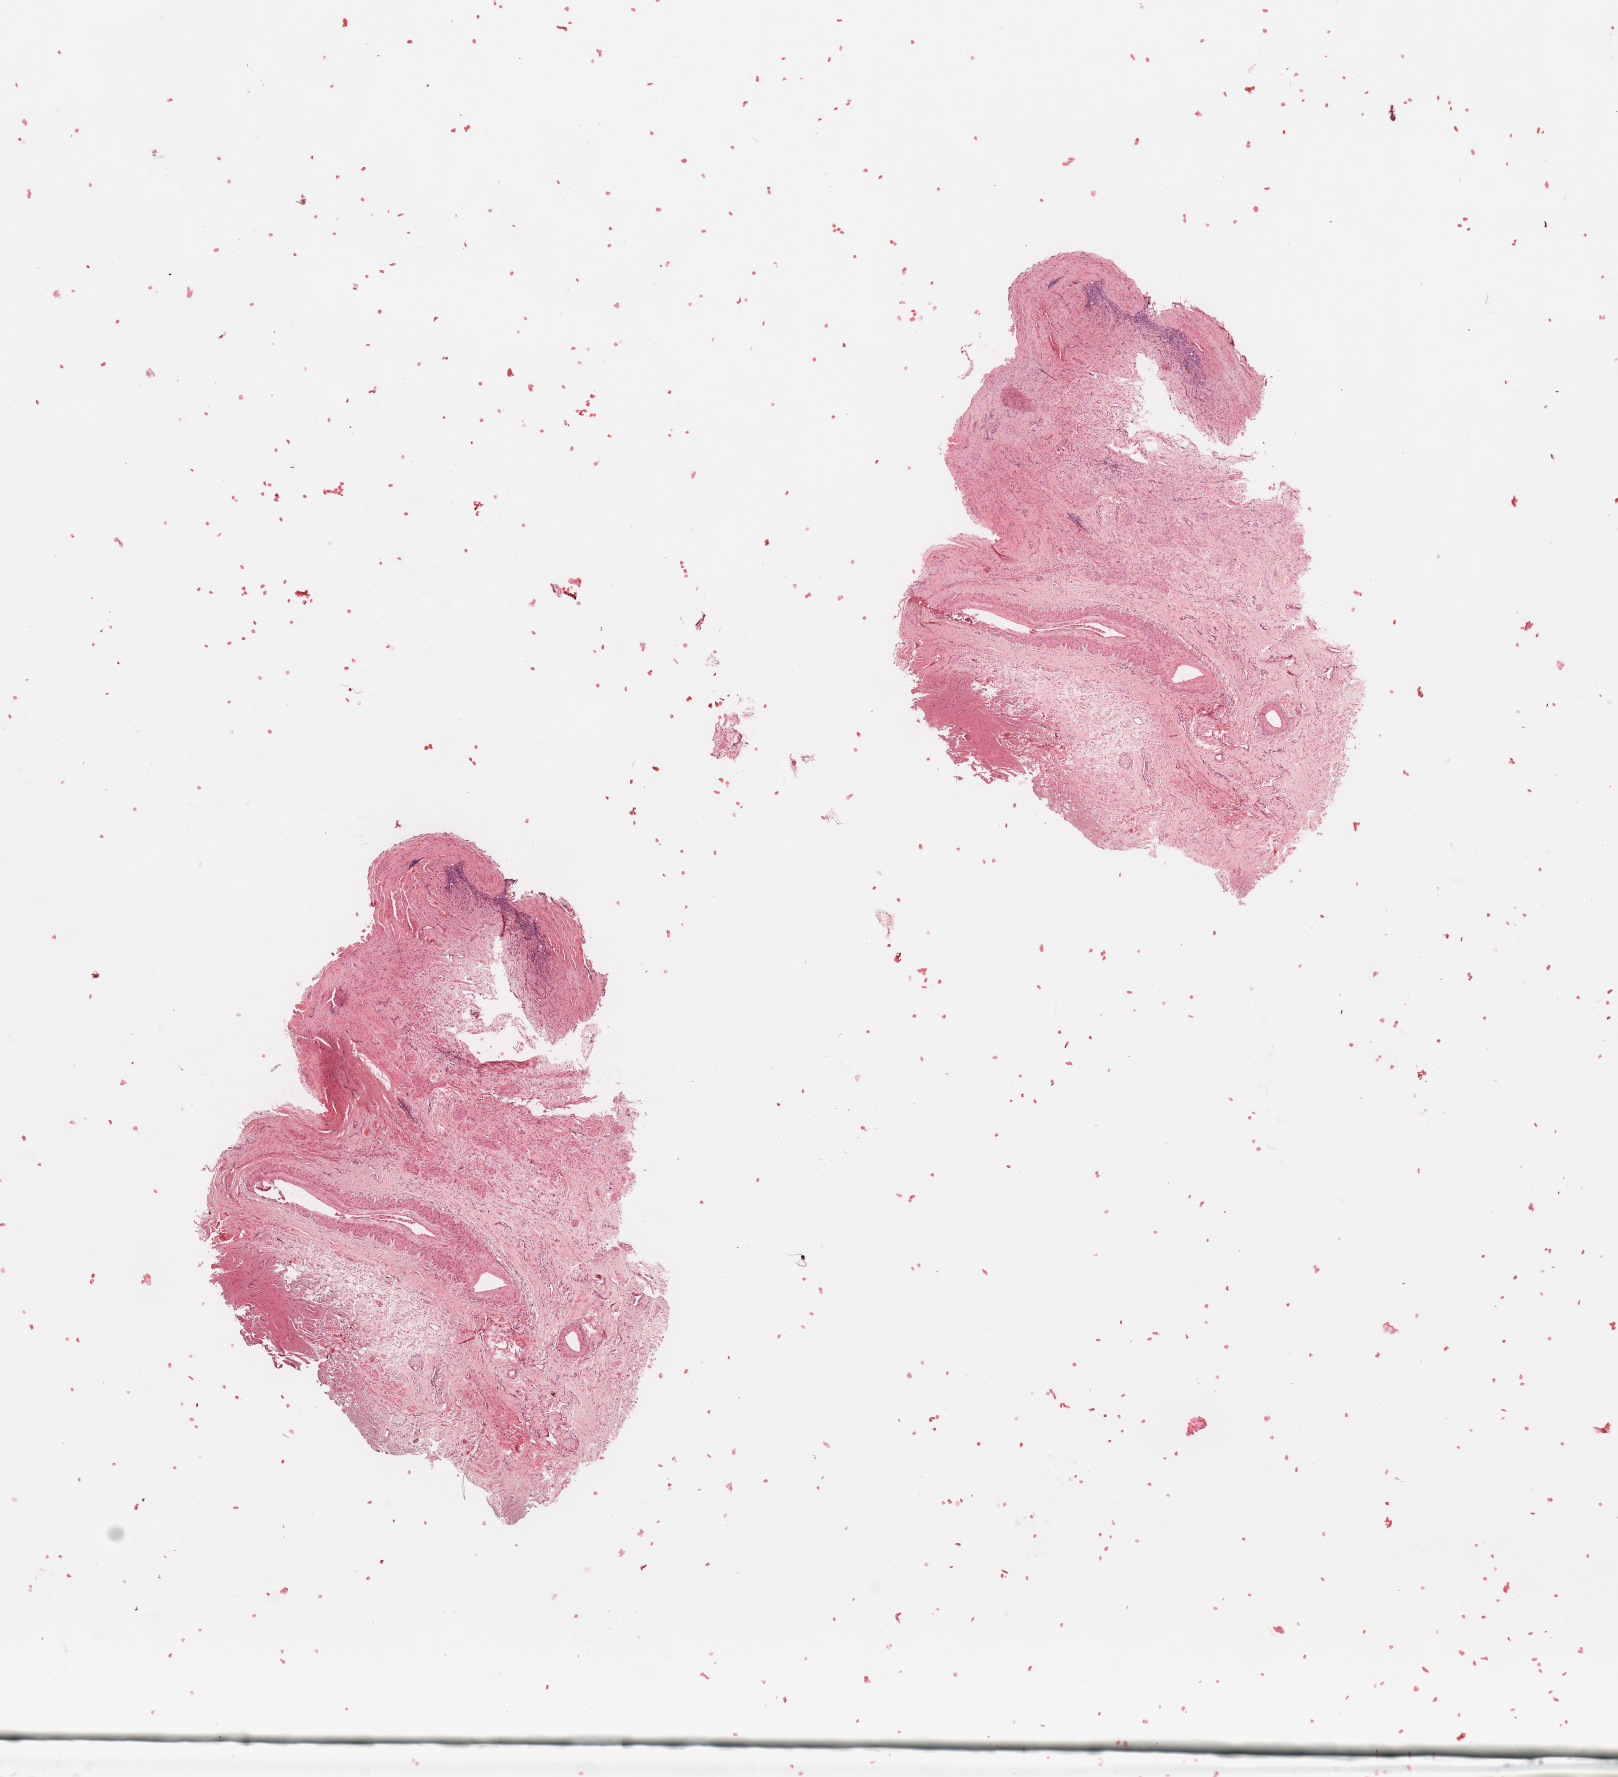
H&E whole-slide image, a low-resolution overview of the entire scanned area, about 12.8 x 14.1 mm; normal (non-tumour) tissue sample, sampled site: uterus. Female, 58 y/o.
This section: normal (non-tumour) tissue from the same patient. Patient diagnosis: Endometrioid adenocarcinoma, NOS.